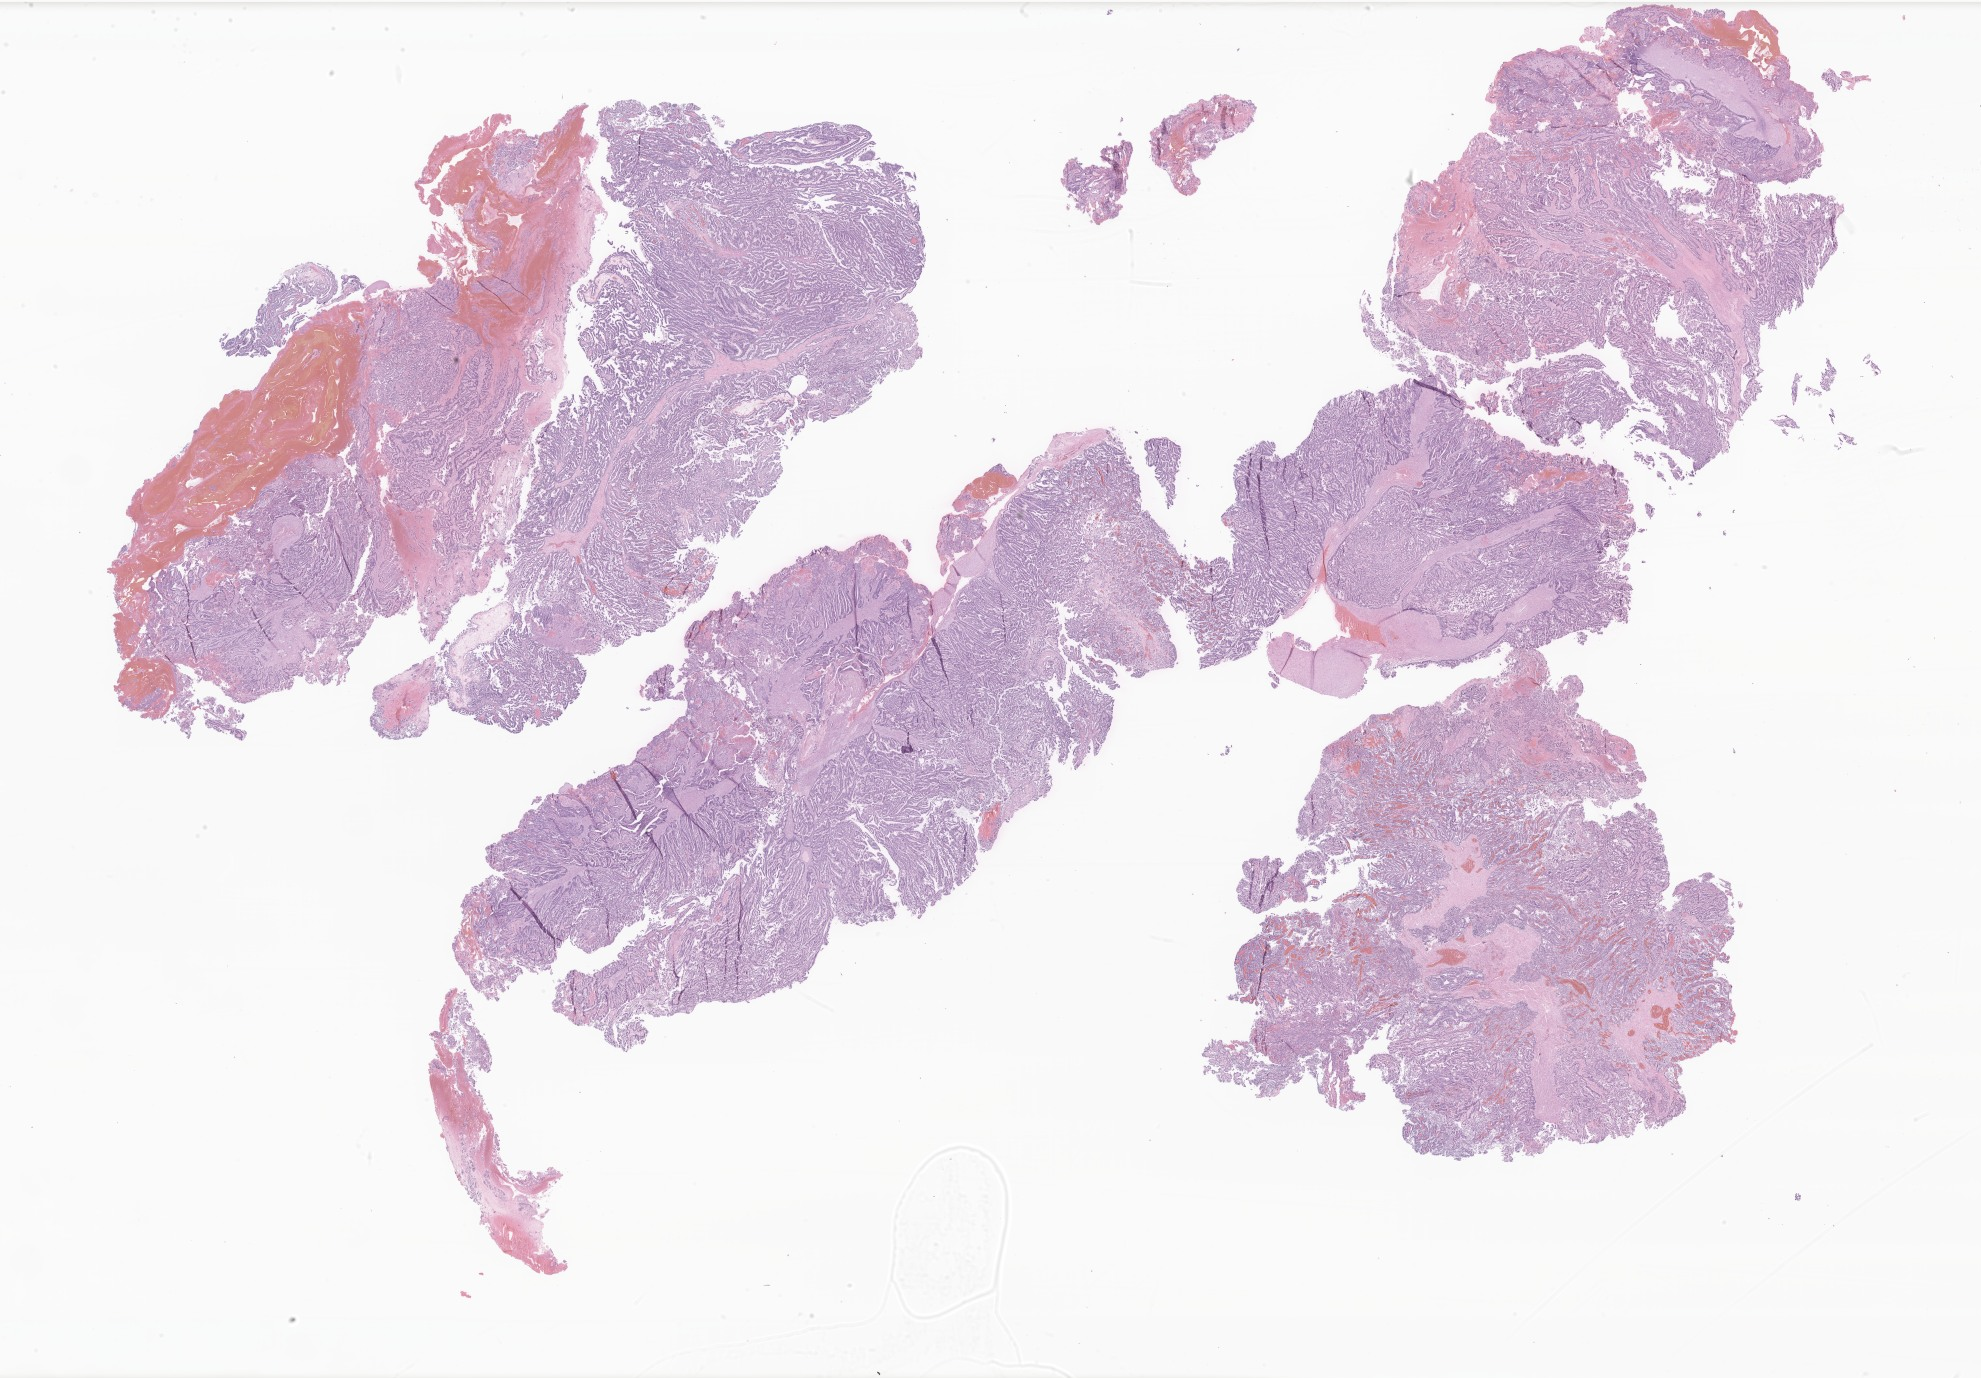
Hematoxylin and eosin (H&E) whole-slide image of tumor tissue from the cerebral ventricle, shown as a low-resolution overview of the whole scanned area (about 33.4 x 23.2 mm); formalin-fixed, paraffin-embedded (FFPE) tissue. Male patient, age 192 days.
* diagnosis: Atypical choroid plexus papilloma